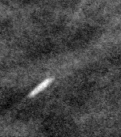
Crop from a digitized film mammogram around one marked abnormality; right breast; MLO view.
Finding: calcifications, morphology lucent center; BI-RADS assessment category 2; subtlety rating 3 on a 1 (subtle) to 5 (obvious) scale; benign; no additional work-up was recommended (benign without callback).